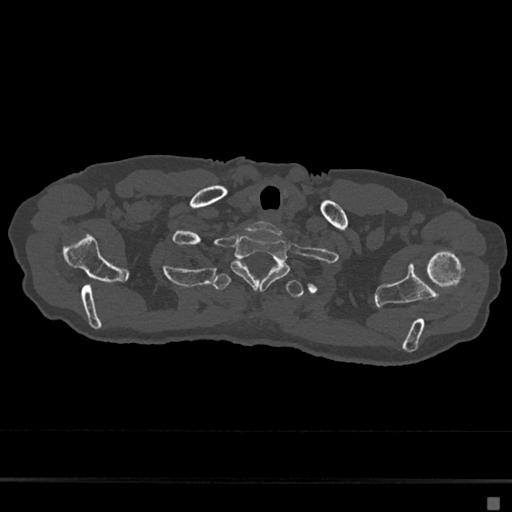
CT including the spine, one axial slice. Position 602 of 797 along the scan axis. Reconstruction kernel Br40s/3. Bone window (W 1800 / L 400 HU). 512 × 512 image matrix, field of view 360 × 360 mm. Female patient, age 68 years. Case-level facts recorded for this patient, not image findings: primary cancer: renal.
Structures marked on this image (semi-automatically segmented with operator editing):
- T1 vertebra: box from (x=231, y=235) to (x=290, y=291) px
- T2 vertebra: (x=212, y=273)–(x=304, y=298)